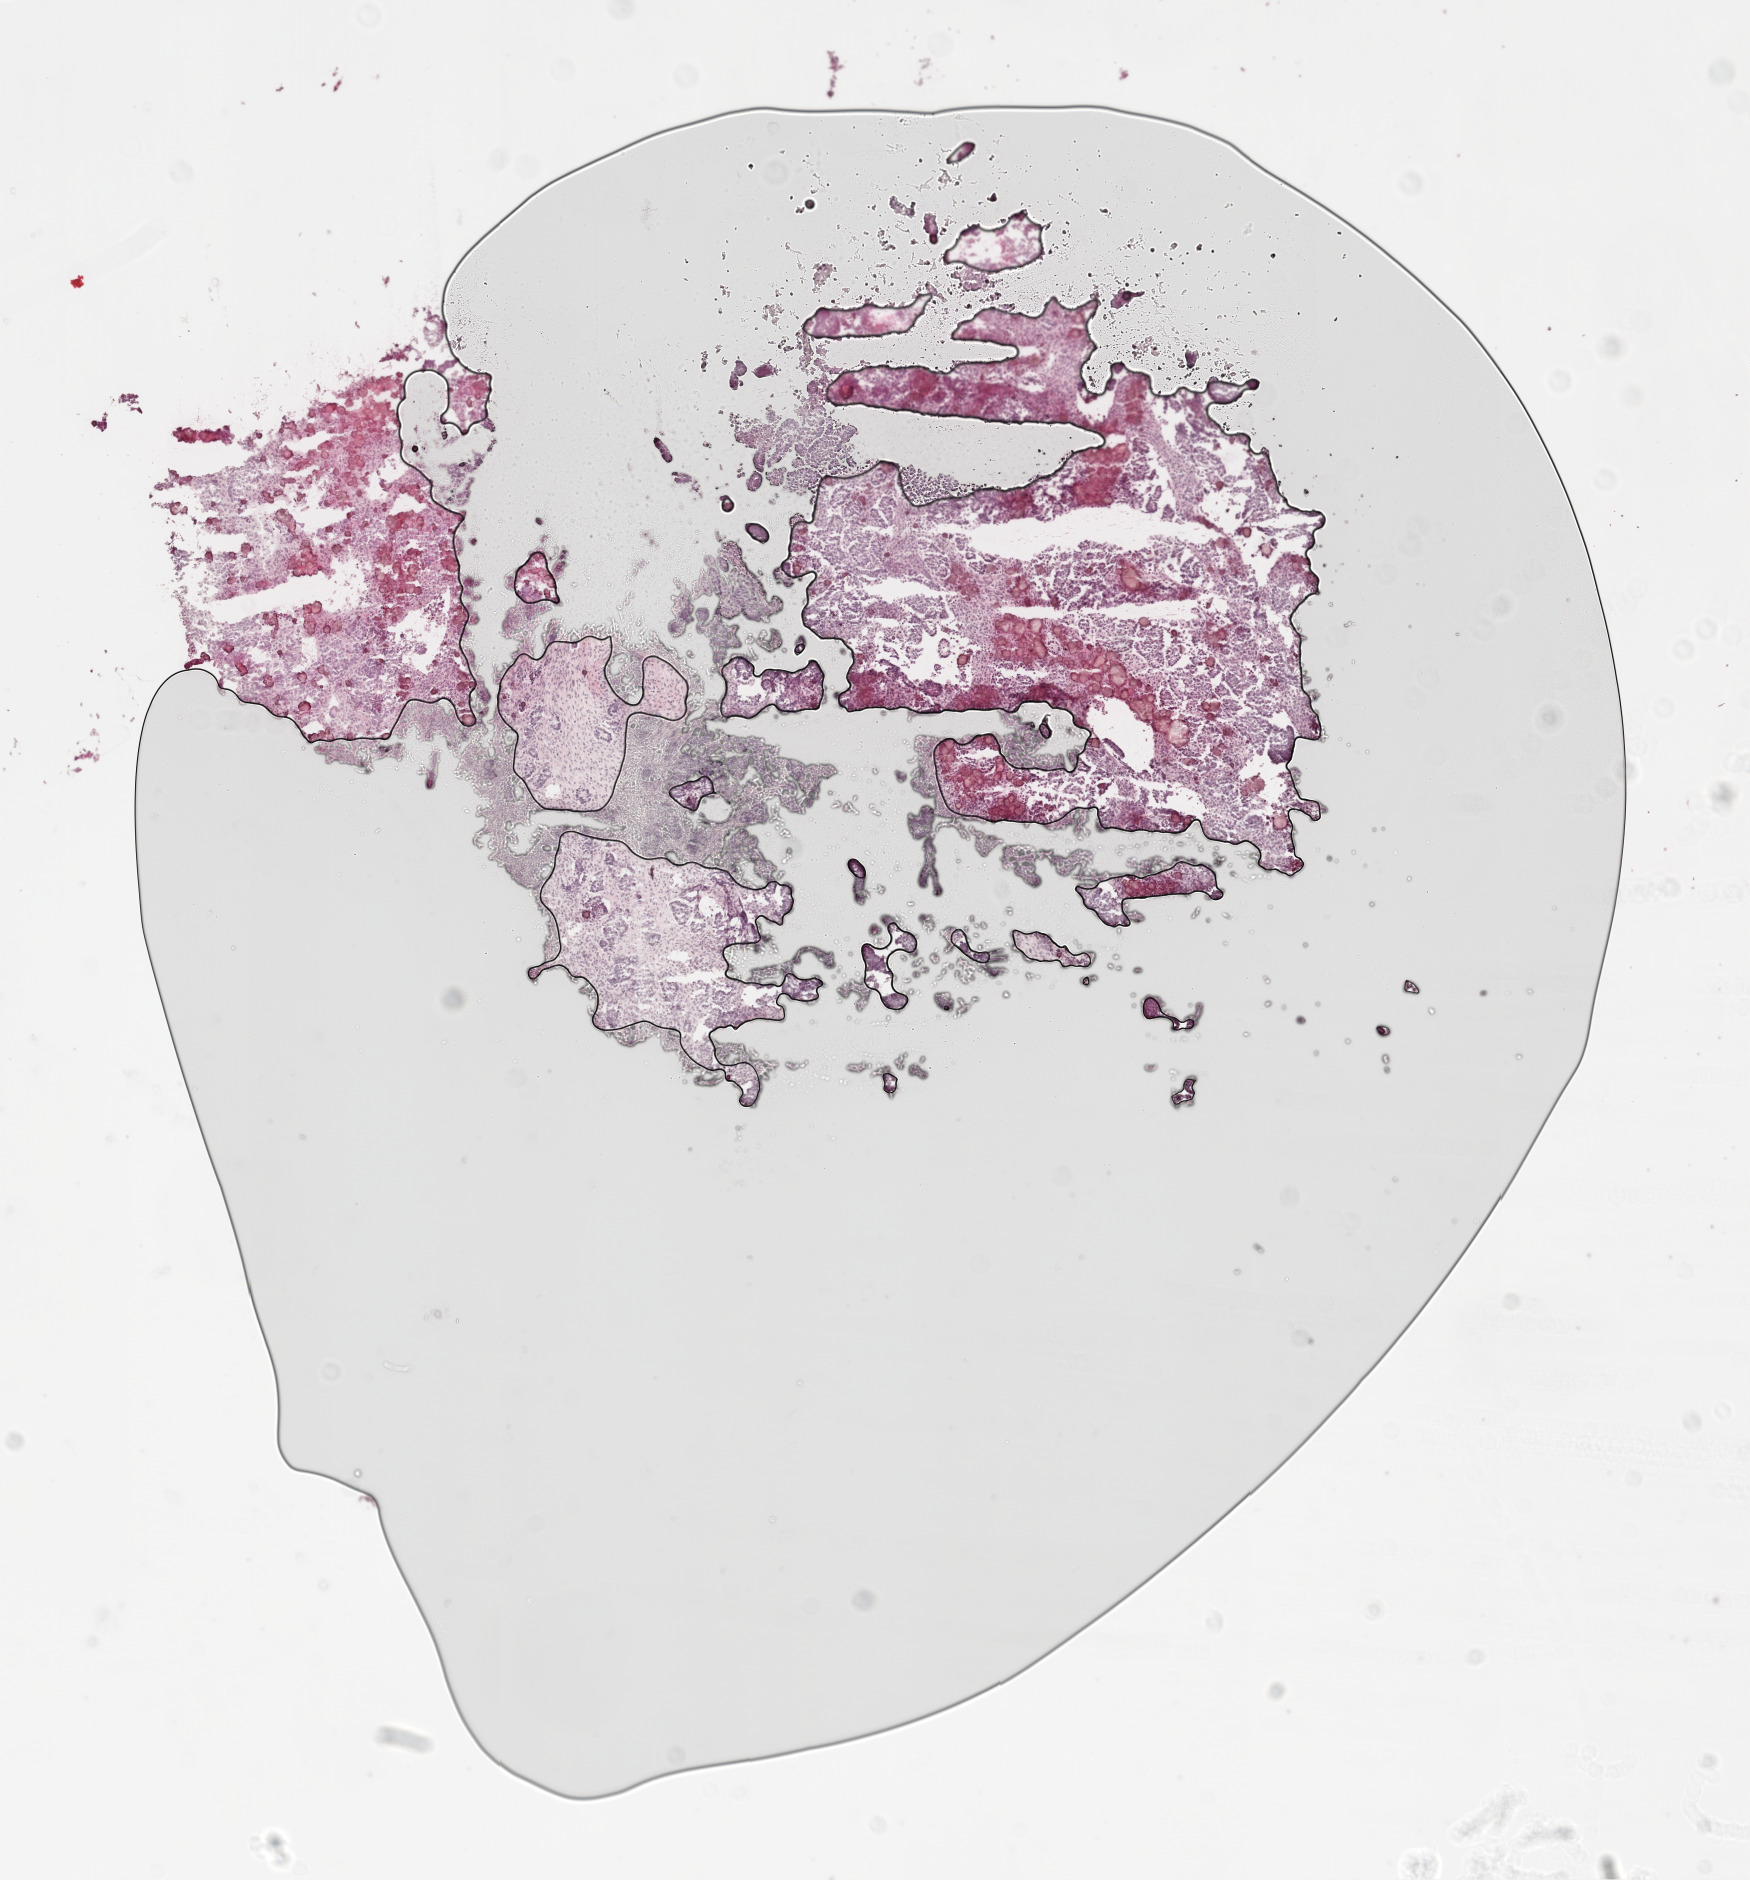
Whole-slide histology image, H&E — a low-resolution overview of the entire scanned area, about 7.0 x 7.5 mm. Frozen section from the top of the tissue portion. Primary tumour sample from the ovary. Patient: female, age at initial diagnosis 46 years. Histologic grade: GX (grade cannot be assessed). Composition of this section per pathologist review: tumour cells 75%, tumour nuclei 80%, normal cells 0%, stromal cells 25%, necrosis 0%.
- histologic diagnosis: Serous cystadenocarcinoma, NOS
- FIGO stage: IV